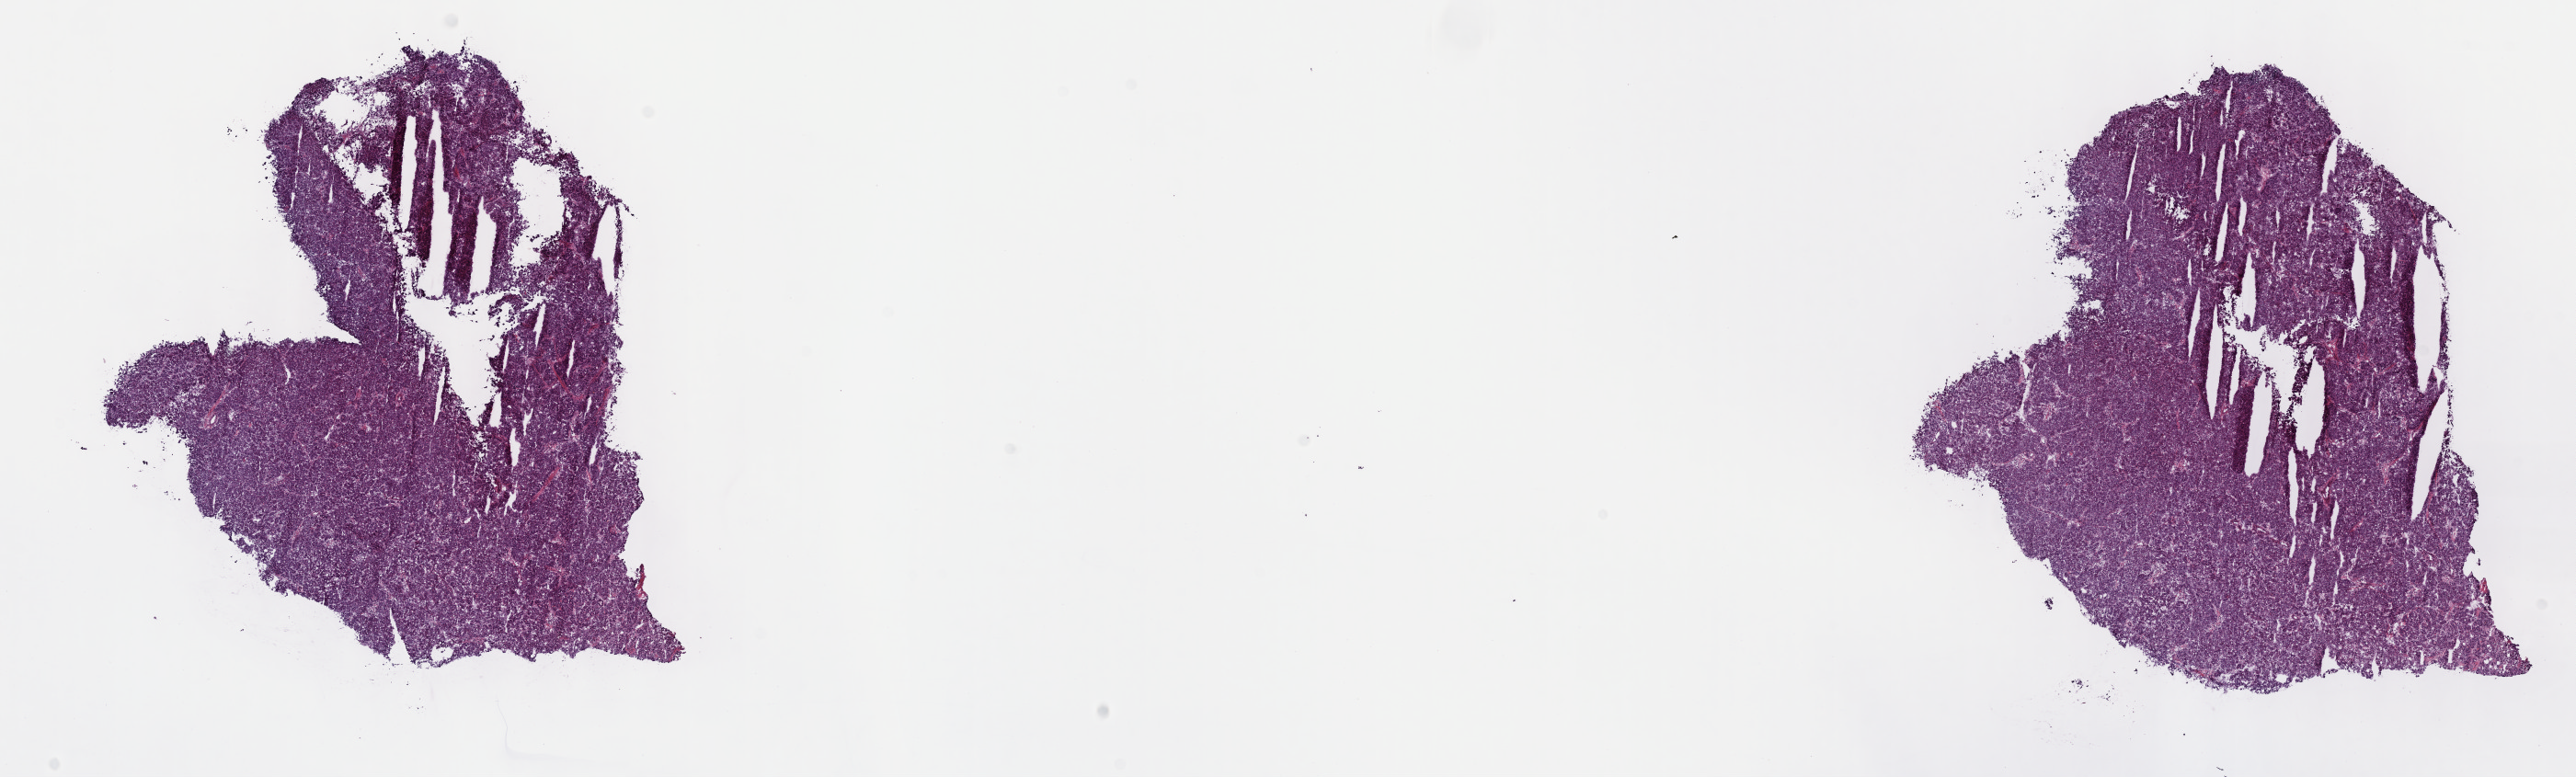
Whole-slide histology image, H&E, whole scanned area (about 22.7 x 6.8 mm) shown as a low-resolution overview. Frozen section from the top of the tissue portion. Sample: primary tumour, liver. Male patient; age at initial diagnosis 44 years. Histologic grade: G2 (moderately differentiated). Pathologist review of this section (percent, as recorded): tumour cells 80%, tumour nuclei 80%, normal cells 0%, stromal cells 20%, necrosis 0%. Inflammatory infiltration, as recorded: lymphocyte infiltration 3%, monocyte infiltration 1%, neutrophil infiltration 3%.
• pathologic diagnosis: Hepatocellular carcinoma, NOS
• AJCC pathologic stage: I (6th edition)